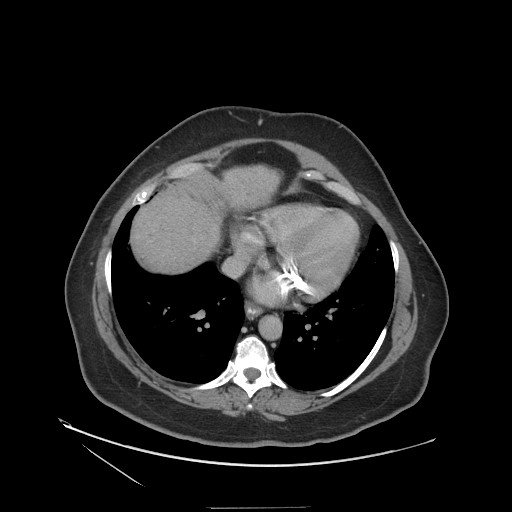
Contrast-enhanced abdominal CT (liver protocol), one axial slice; slice 107 of 127 in the series (ordered by position); reconstruction kernel STANDARD; 140 kVp; soft-tissue window (W 400 / L 40 HU); 2.5 mm slice thickness; 512 × 512 image matrix, field of view 480 × 480 mm. Case-level facts recorded for this patient, not image findings: diagnosis: hepatocellular carcinoma (patient treated with transarterial chemoembolisation; whether this scan precedes or follows treatment is not stated here); TNM stage (as recorded): Stage-II; Child-Pugh class: A; tumour differentiation: well differentiated; tumour nodularity: multinodular.
Annotated regions visible in this slice (semi-automatically segmented with operator editing):
- liver parenchyma outside the tumour (the mass and vessels are separate outlines, so this box may not span the whole liver): bounding box [x1, y1, x2, y2] px = [132, 166, 279, 272]